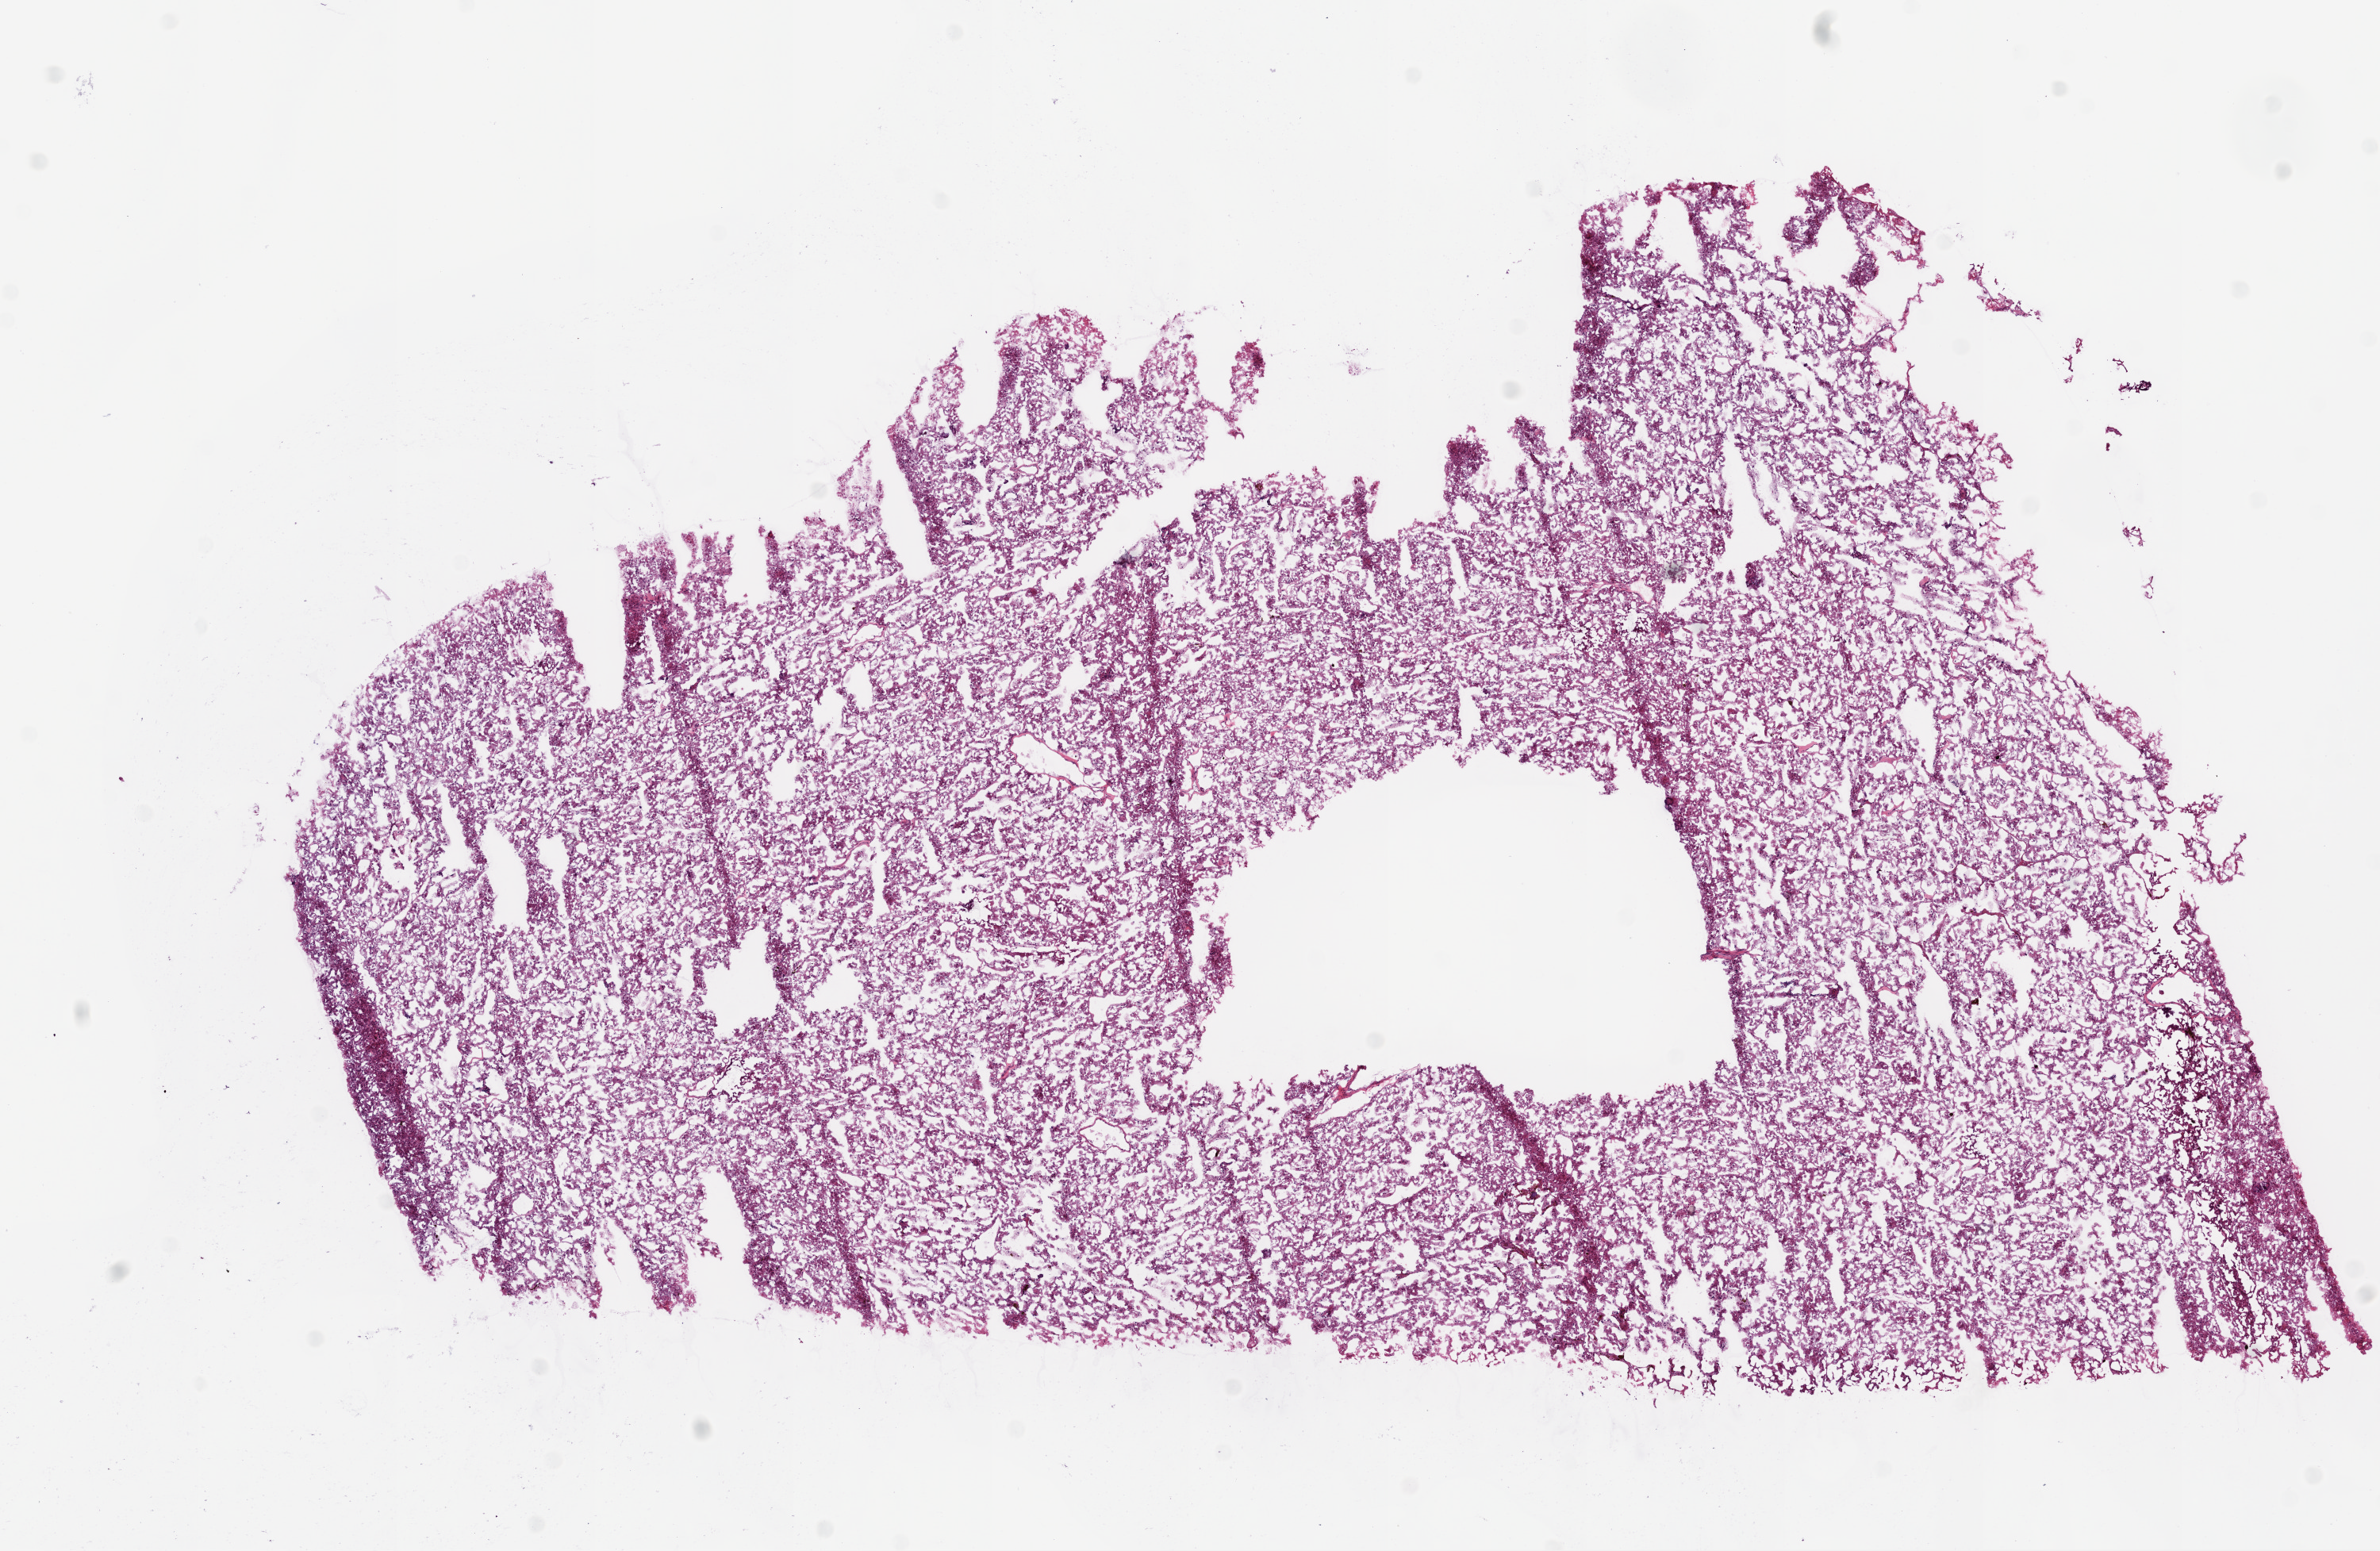
Digitized H&E-stained tissue section (whole slide) — whole scanned area (about 12.0 x 7.8 mm) shown as a low-resolution overview, frozen section, sample: primary tumour, kidney. Male, age 58 years at initial diagnosis. Pathologist review of this section (percent, as recorded): tumour nuclei 85%, normal cells 0%.
Pathologic diagnosis: Clear cell adenocarcinoma, NOS.